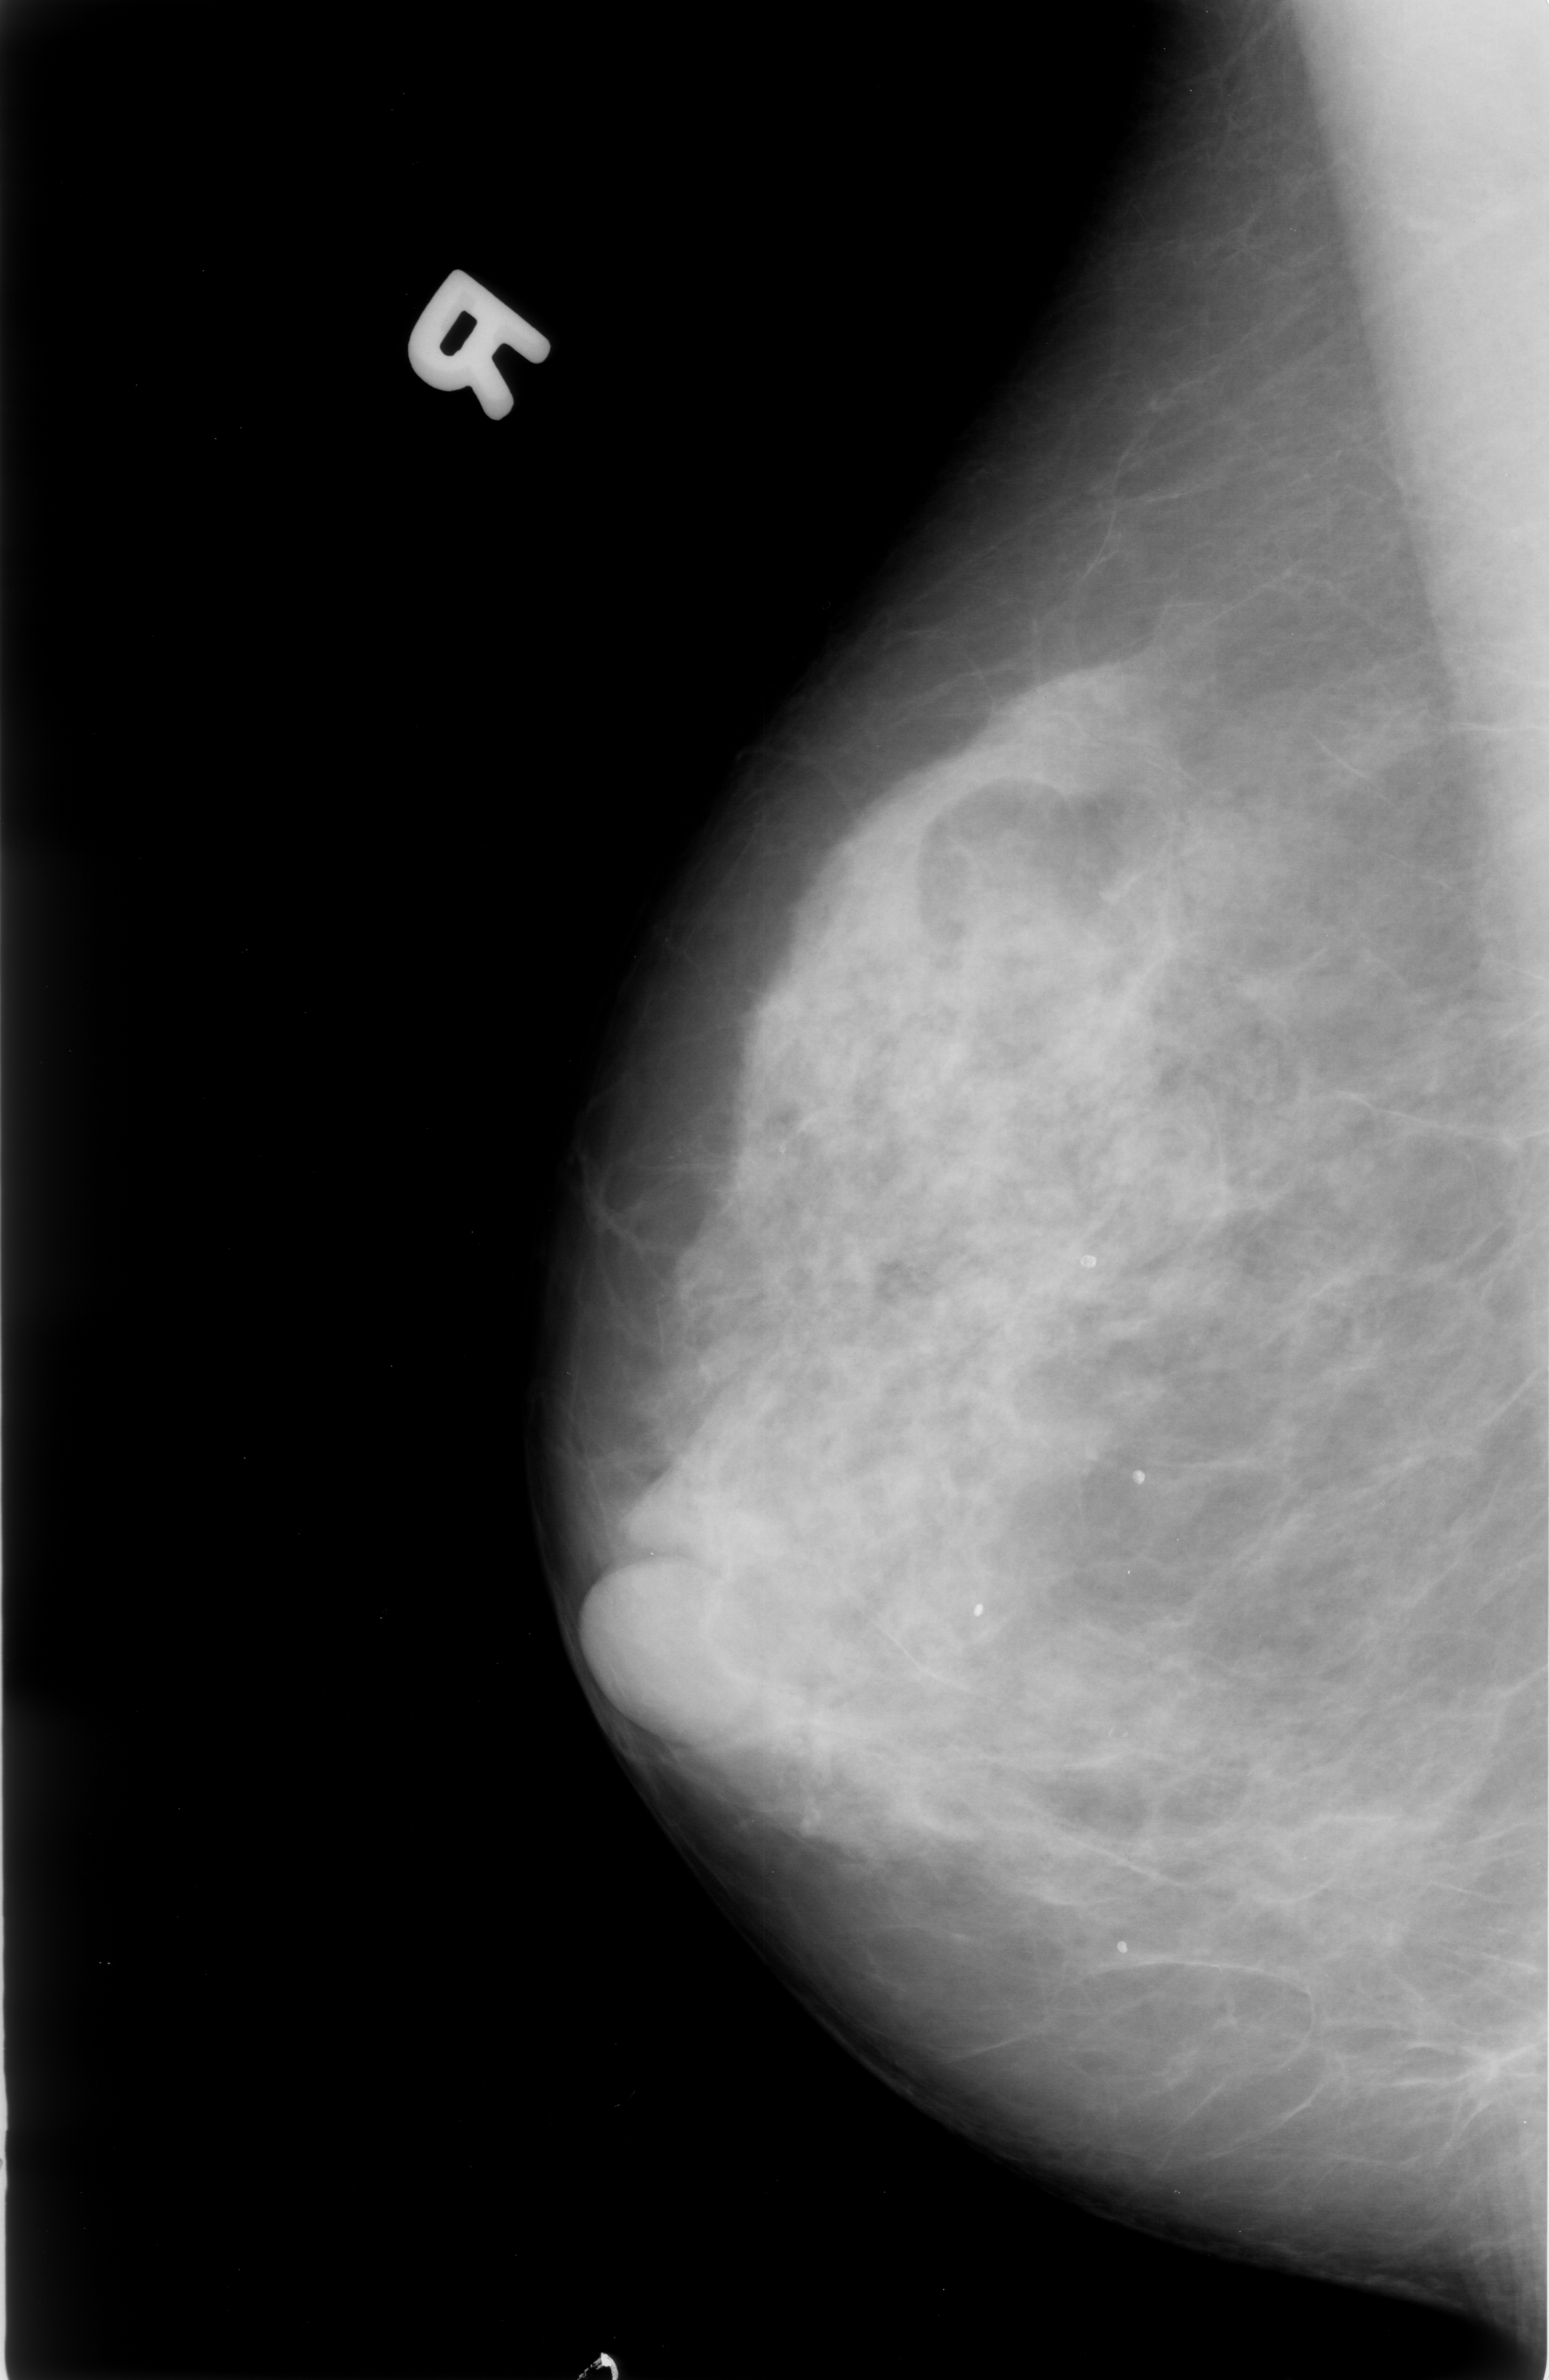
Mammogram (digitized film), right breast, mediolateral oblique (MLO) view, breast composition: heterogeneously dense (BI-RADS density category 3 of 4).
- Marked abnormality: calcifications, morphology punctate / pleomorphic, distribution clustered; BI-RADS assessment category 3; pathology result (as recorded, not read from the image): malignant.